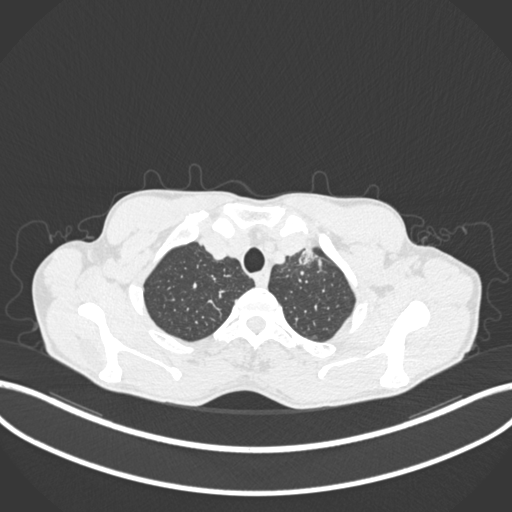
Chest CT, one axial slice; slice 182 of 211 in the series (ordered by position); 120 kVp; lung window (W 1500 / L -600 HU); 1 mm slice thickness; 512 × 512 image matrix, field of view 400 × 400 mm. Patient: male, 58 years. From the clinical record (not read from this slice): clinical TNM (as recorded): T1c N1 M0.
Outlined on this slice (bounding box drawn by a radiologist):
- lung tumour (recorded histology: adenocarcinoma): bounding box (x1, y1, x2, y2) in pixels: (297, 238, 323, 270)